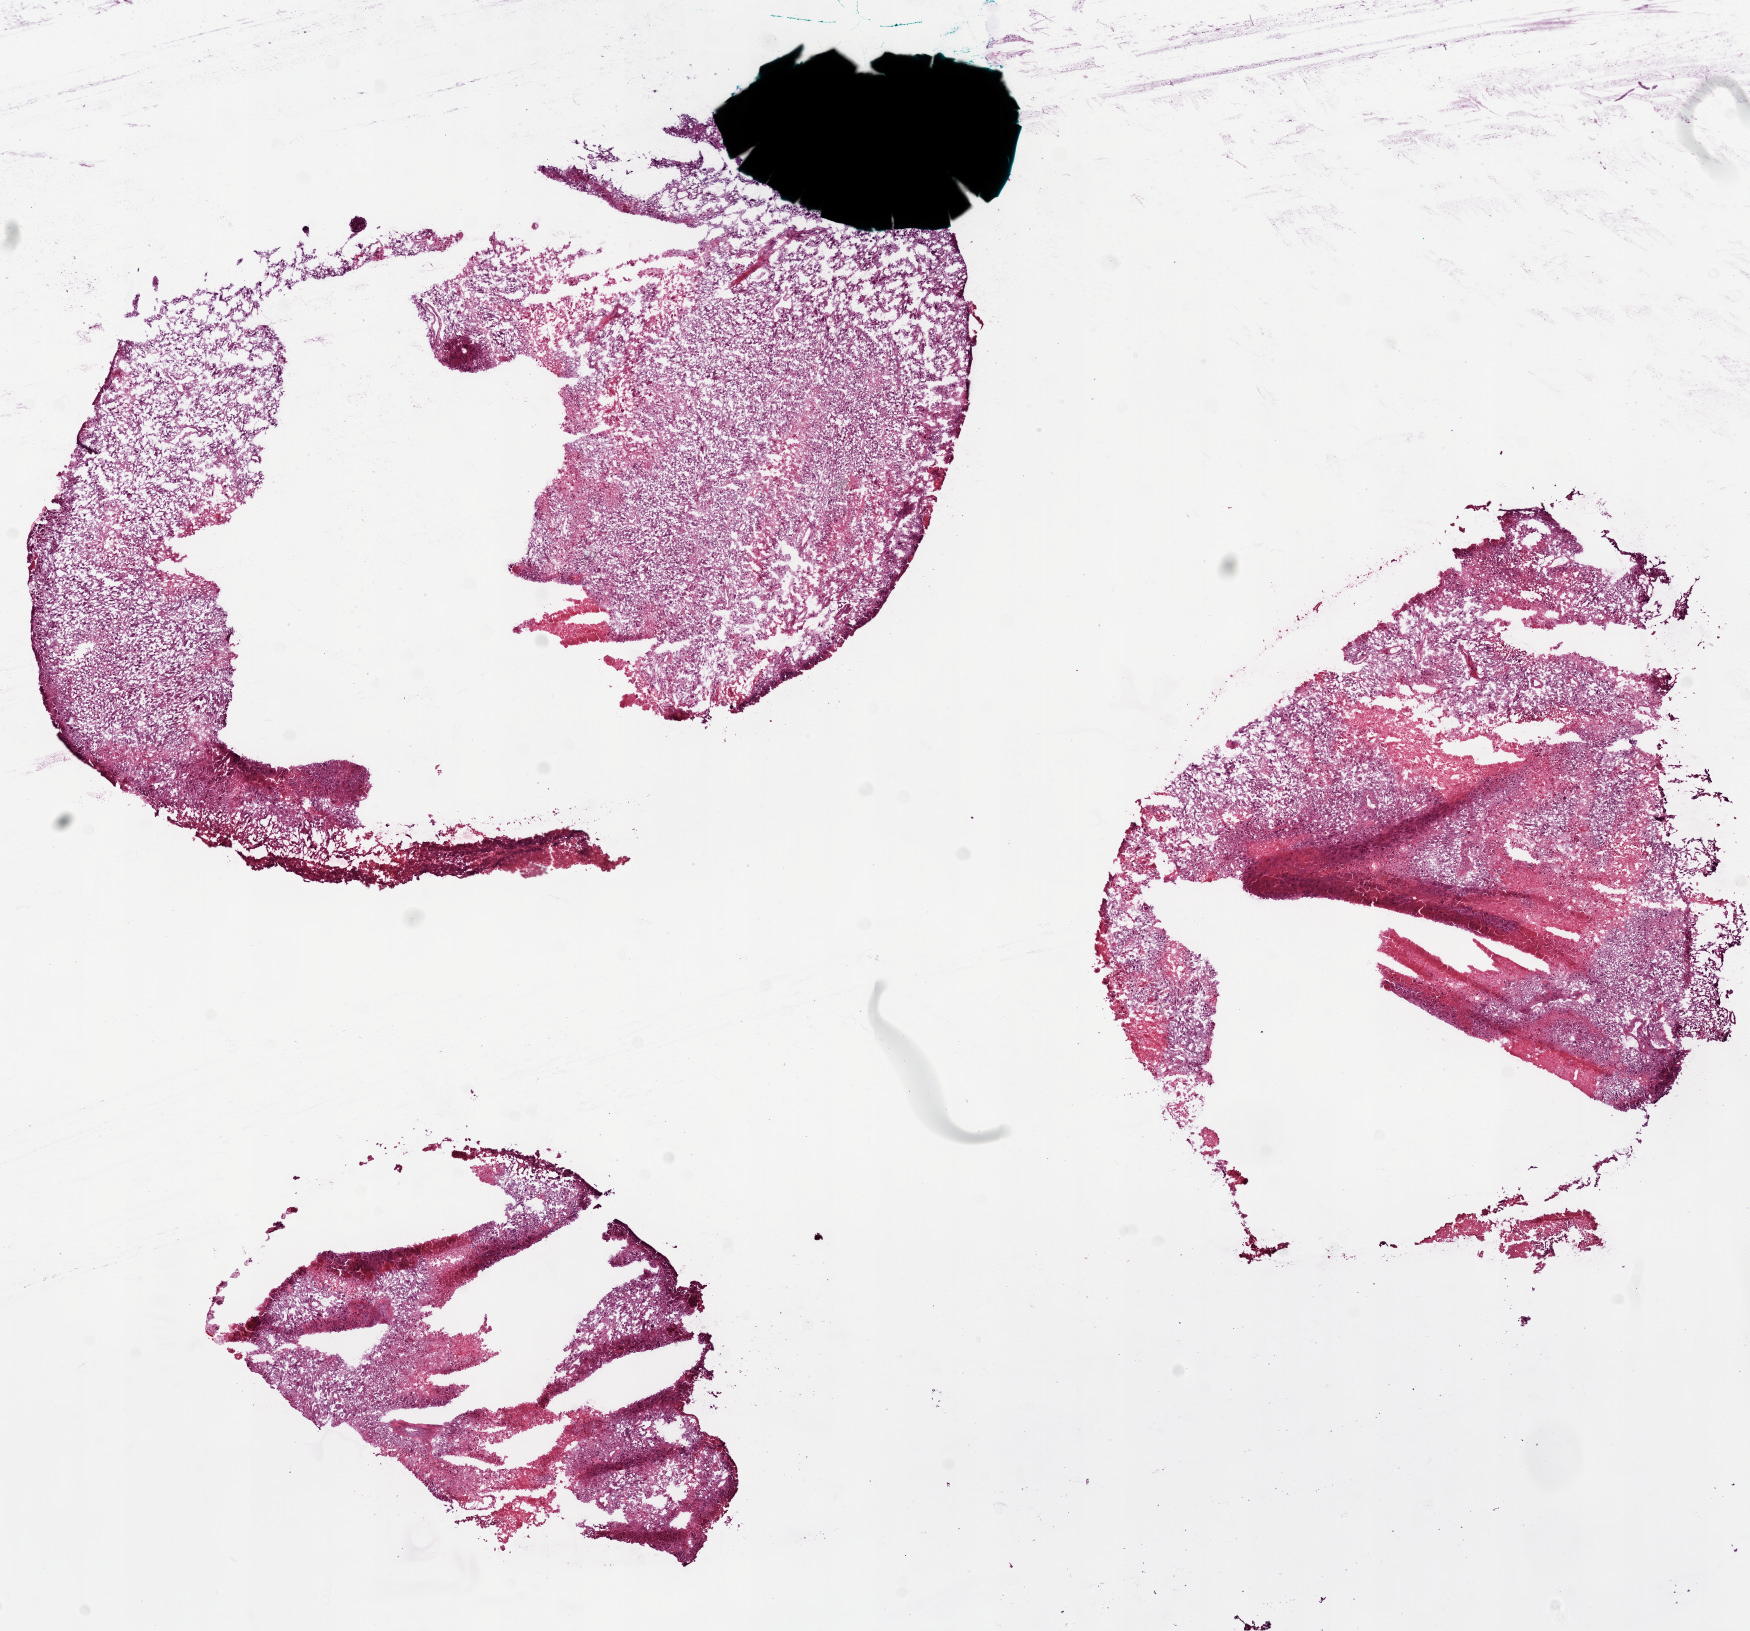
Hematoxylin and eosin (H&E) stained whole-slide image — a low-resolution overview of the entire scanned area, about 14.0 x 13.1 mm (from a 20x scan). Frozen section from the bottom of the tissue portion. Primary tumour sample from the brain. Female, age 78 years at initial diagnosis. Pathologist review of this section (percent, as recorded): tumour cells 65%, tumour nuclei 80%, stromal cells 10%, necrosis 25%.
- histologic diagnosis: Glioblastoma